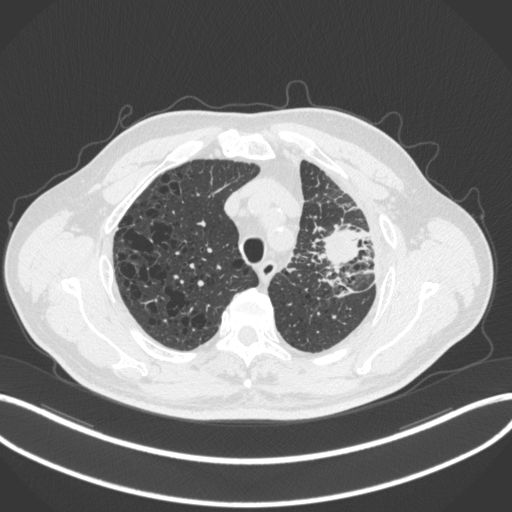
Chest CT, one axial slice; slice 242 of 286 in the series (ordered by position); 120 kVp; lung window (W 1500 / L -600 HU); 1 mm slice thickness; 512 × 512 image matrix, field of view 400 × 400 mm. Male patient, age 68 years. From the clinical record (not read from this slice): clinical TNM (as recorded): T3 N3 M1.
Structures marked on this image (bounding box drawn by a radiologist):
- lung tumour (recorded histology: adenocarcinoma): bounding box (x1, y1, x2, y2) in pixels: (320, 219, 362, 278)